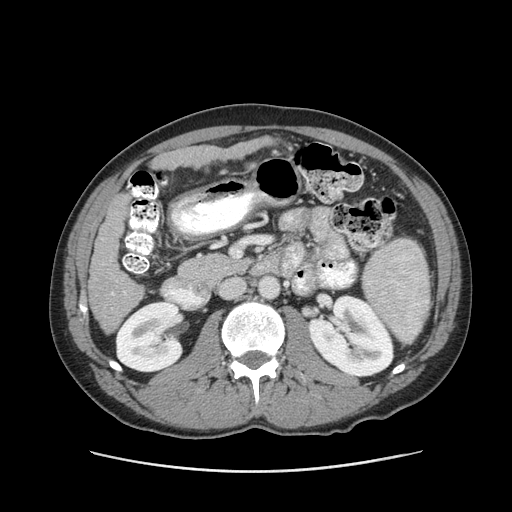
Contrast-enhanced abdominal CT (liver protocol), one axial slice; position 34 of 93 along the scan axis; reconstruction kernel STANDARD; soft-tissue window (W 400 / L 40 HU); 2.5 mm slice thickness; 512 × 512 image matrix. Case-level facts recorded for this patient, not image findings: diagnosis: hepatocellular carcinoma (patient treated with transarterial chemoembolisation; whether this scan precedes or follows treatment is not stated here); TNM stage (as recorded): Stage-II; Child-Pugh class: A; tumour differentiation: moderately differentiated; tumour size: 1 cm.
Outlined on this slice (semi-automatic segmentation, software-assisted and operator-edited):
- liver parenchyma outside the tumour (the mass and vessels are separate outlines, so this box may not span the whole liver): bounding box <88,136,272,333> (left, top, right, bottom; pixels)
- liver vessels: <111,292,126,295>